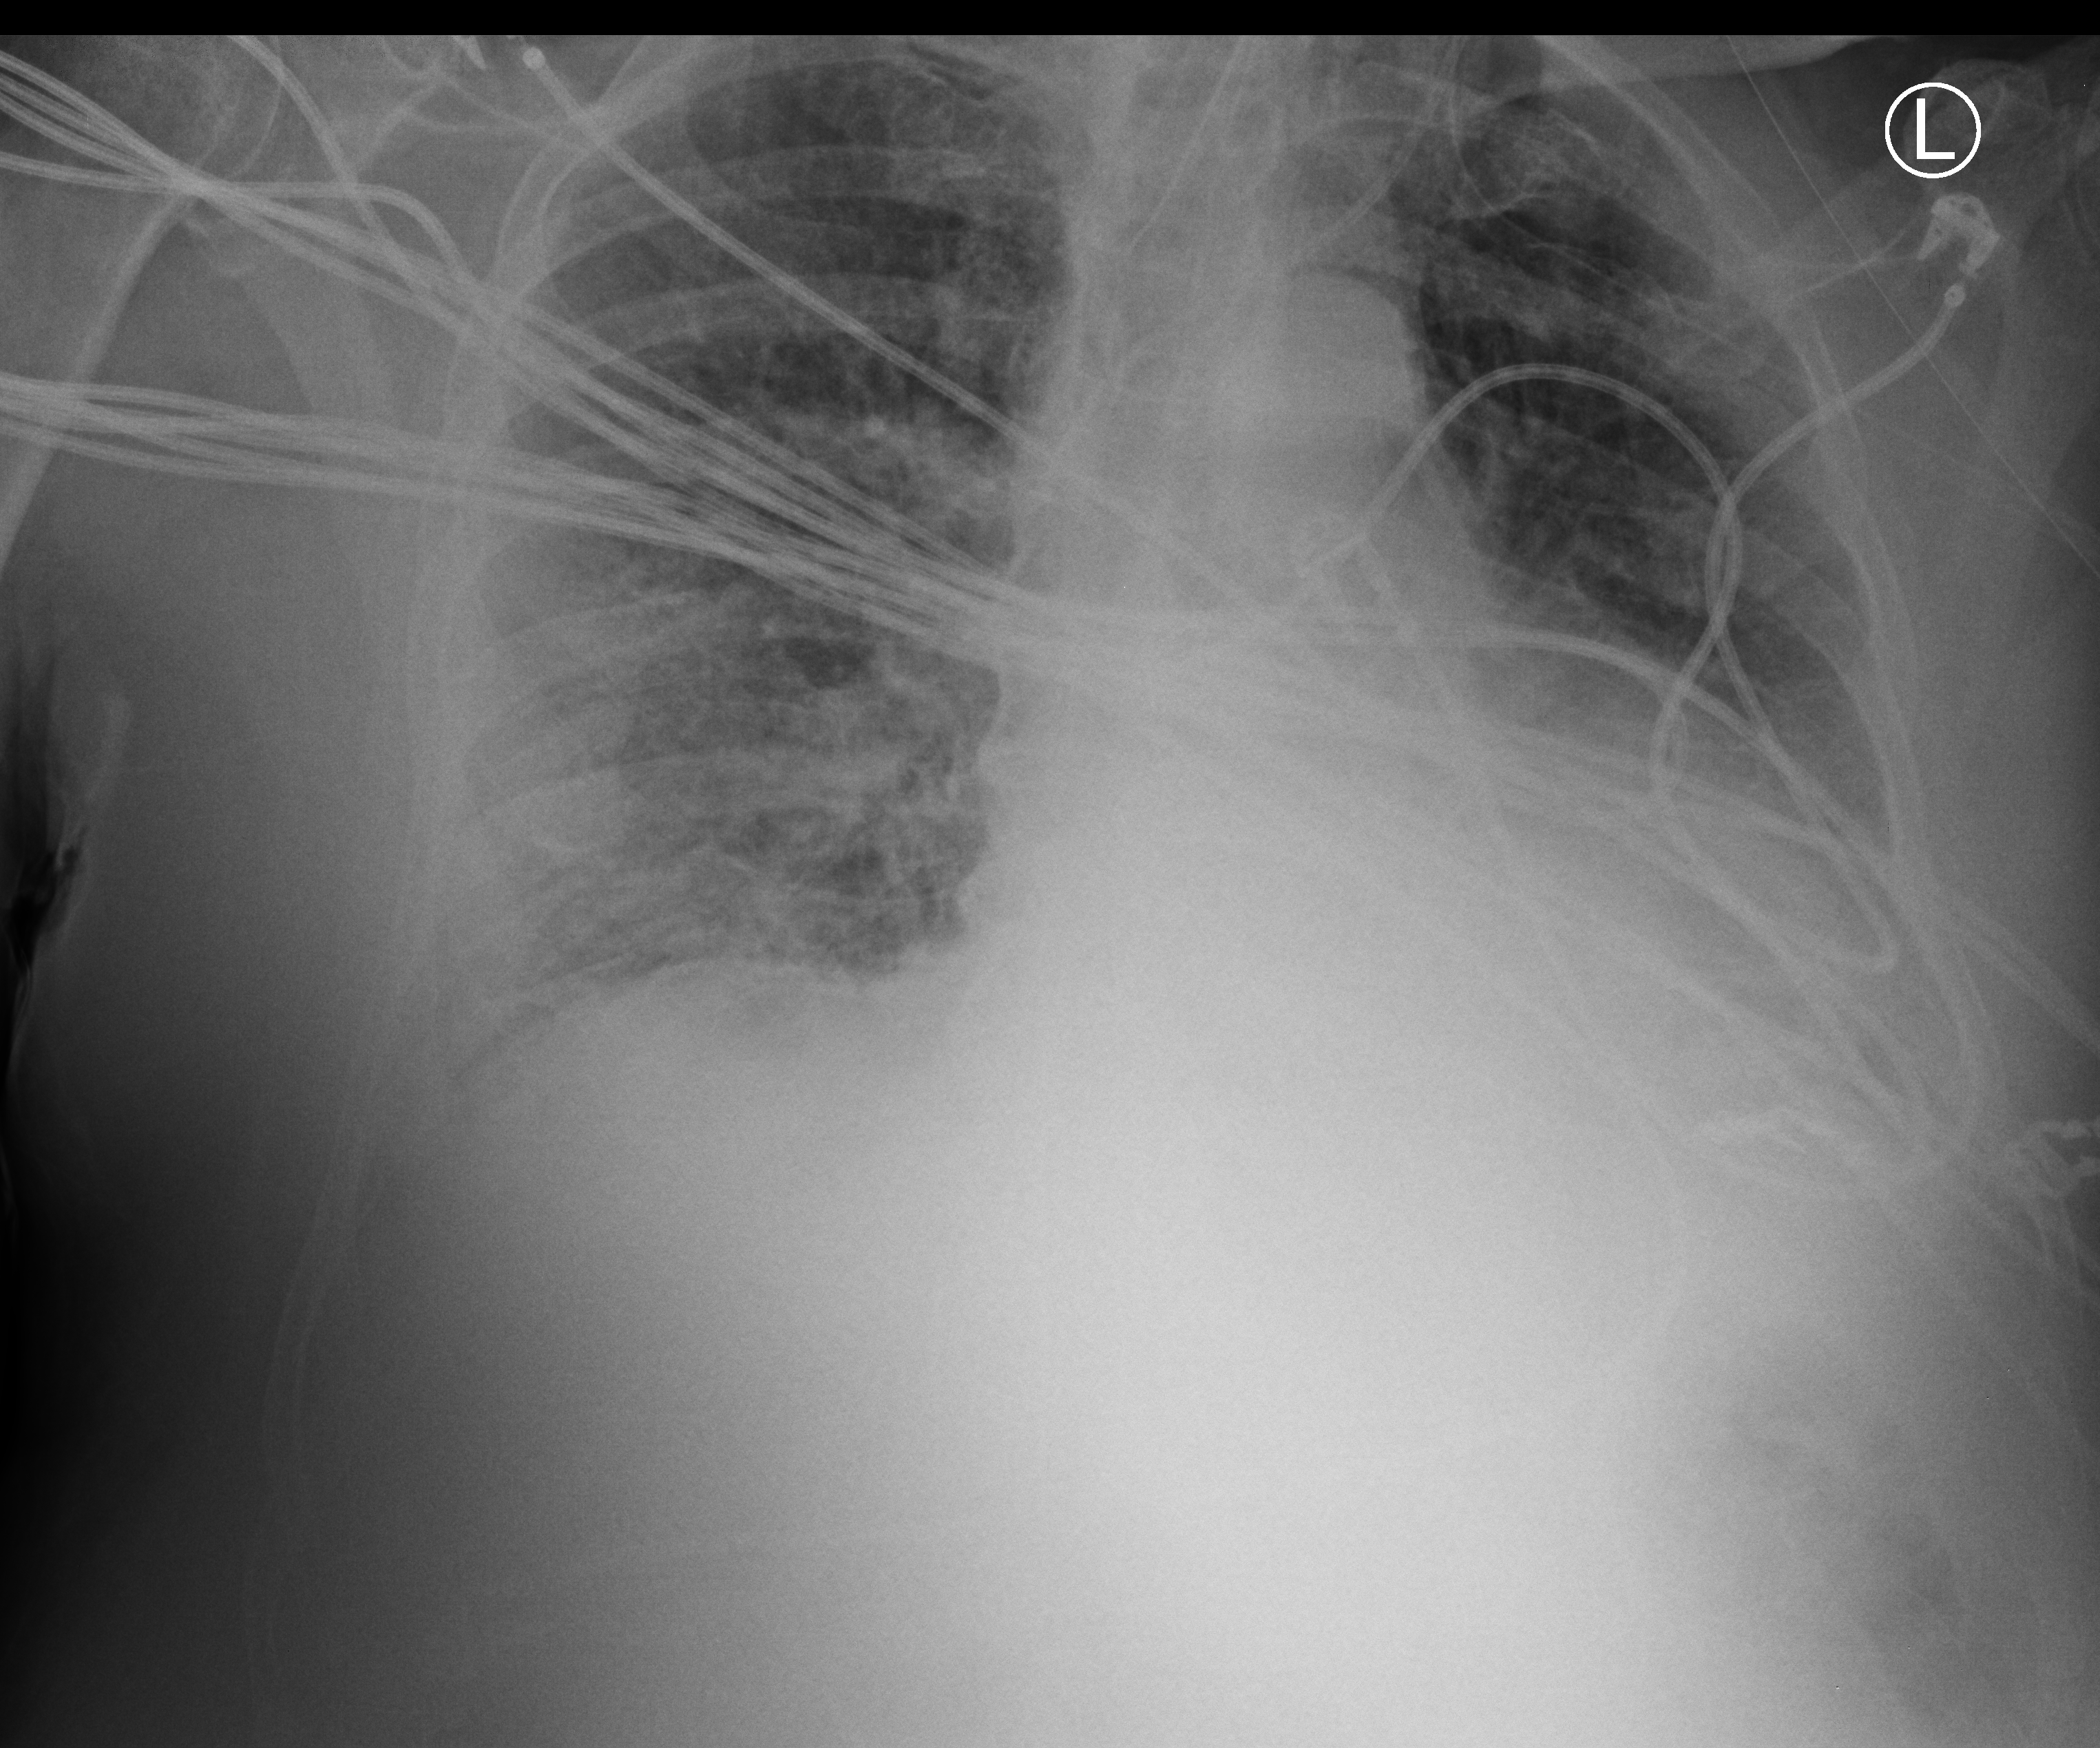
Bedside chest radiograph (computed radiography), anteroposterior (AP) projection. Patient hospitalised with COVID-19; male, aged 75–90 years.
Admission-level facts for this patient (not findings on this image; timing relative to this image not recorded):
- length of hospital stay: 14 days